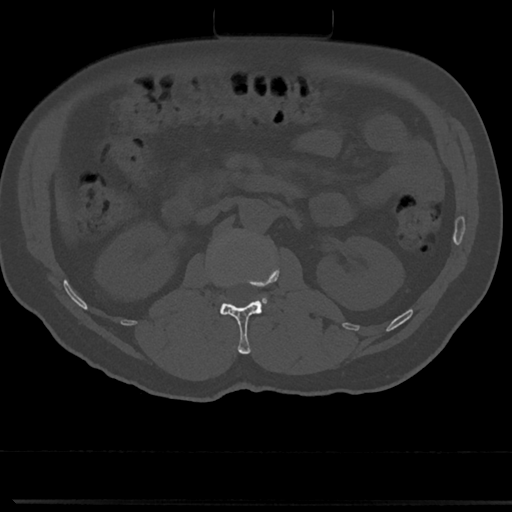
CT including the spine, one axial slice. Slice 56 of 817 in the series (ordered by position). Bone window (W 1800 / L 400 HU). 0.5 mm slice thickness. 512 × 512 image matrix, field of view 355 × 355 mm. Patient: male, 61 years. Case-level facts recorded for this patient, not image findings: primary cancer: prostate.
Structures marked on this image (semi-automatically segmented with operator editing):
- L1 vertebra: bounding box (x1, y1, x2, y2) in pixels: (219, 261, 280, 354)